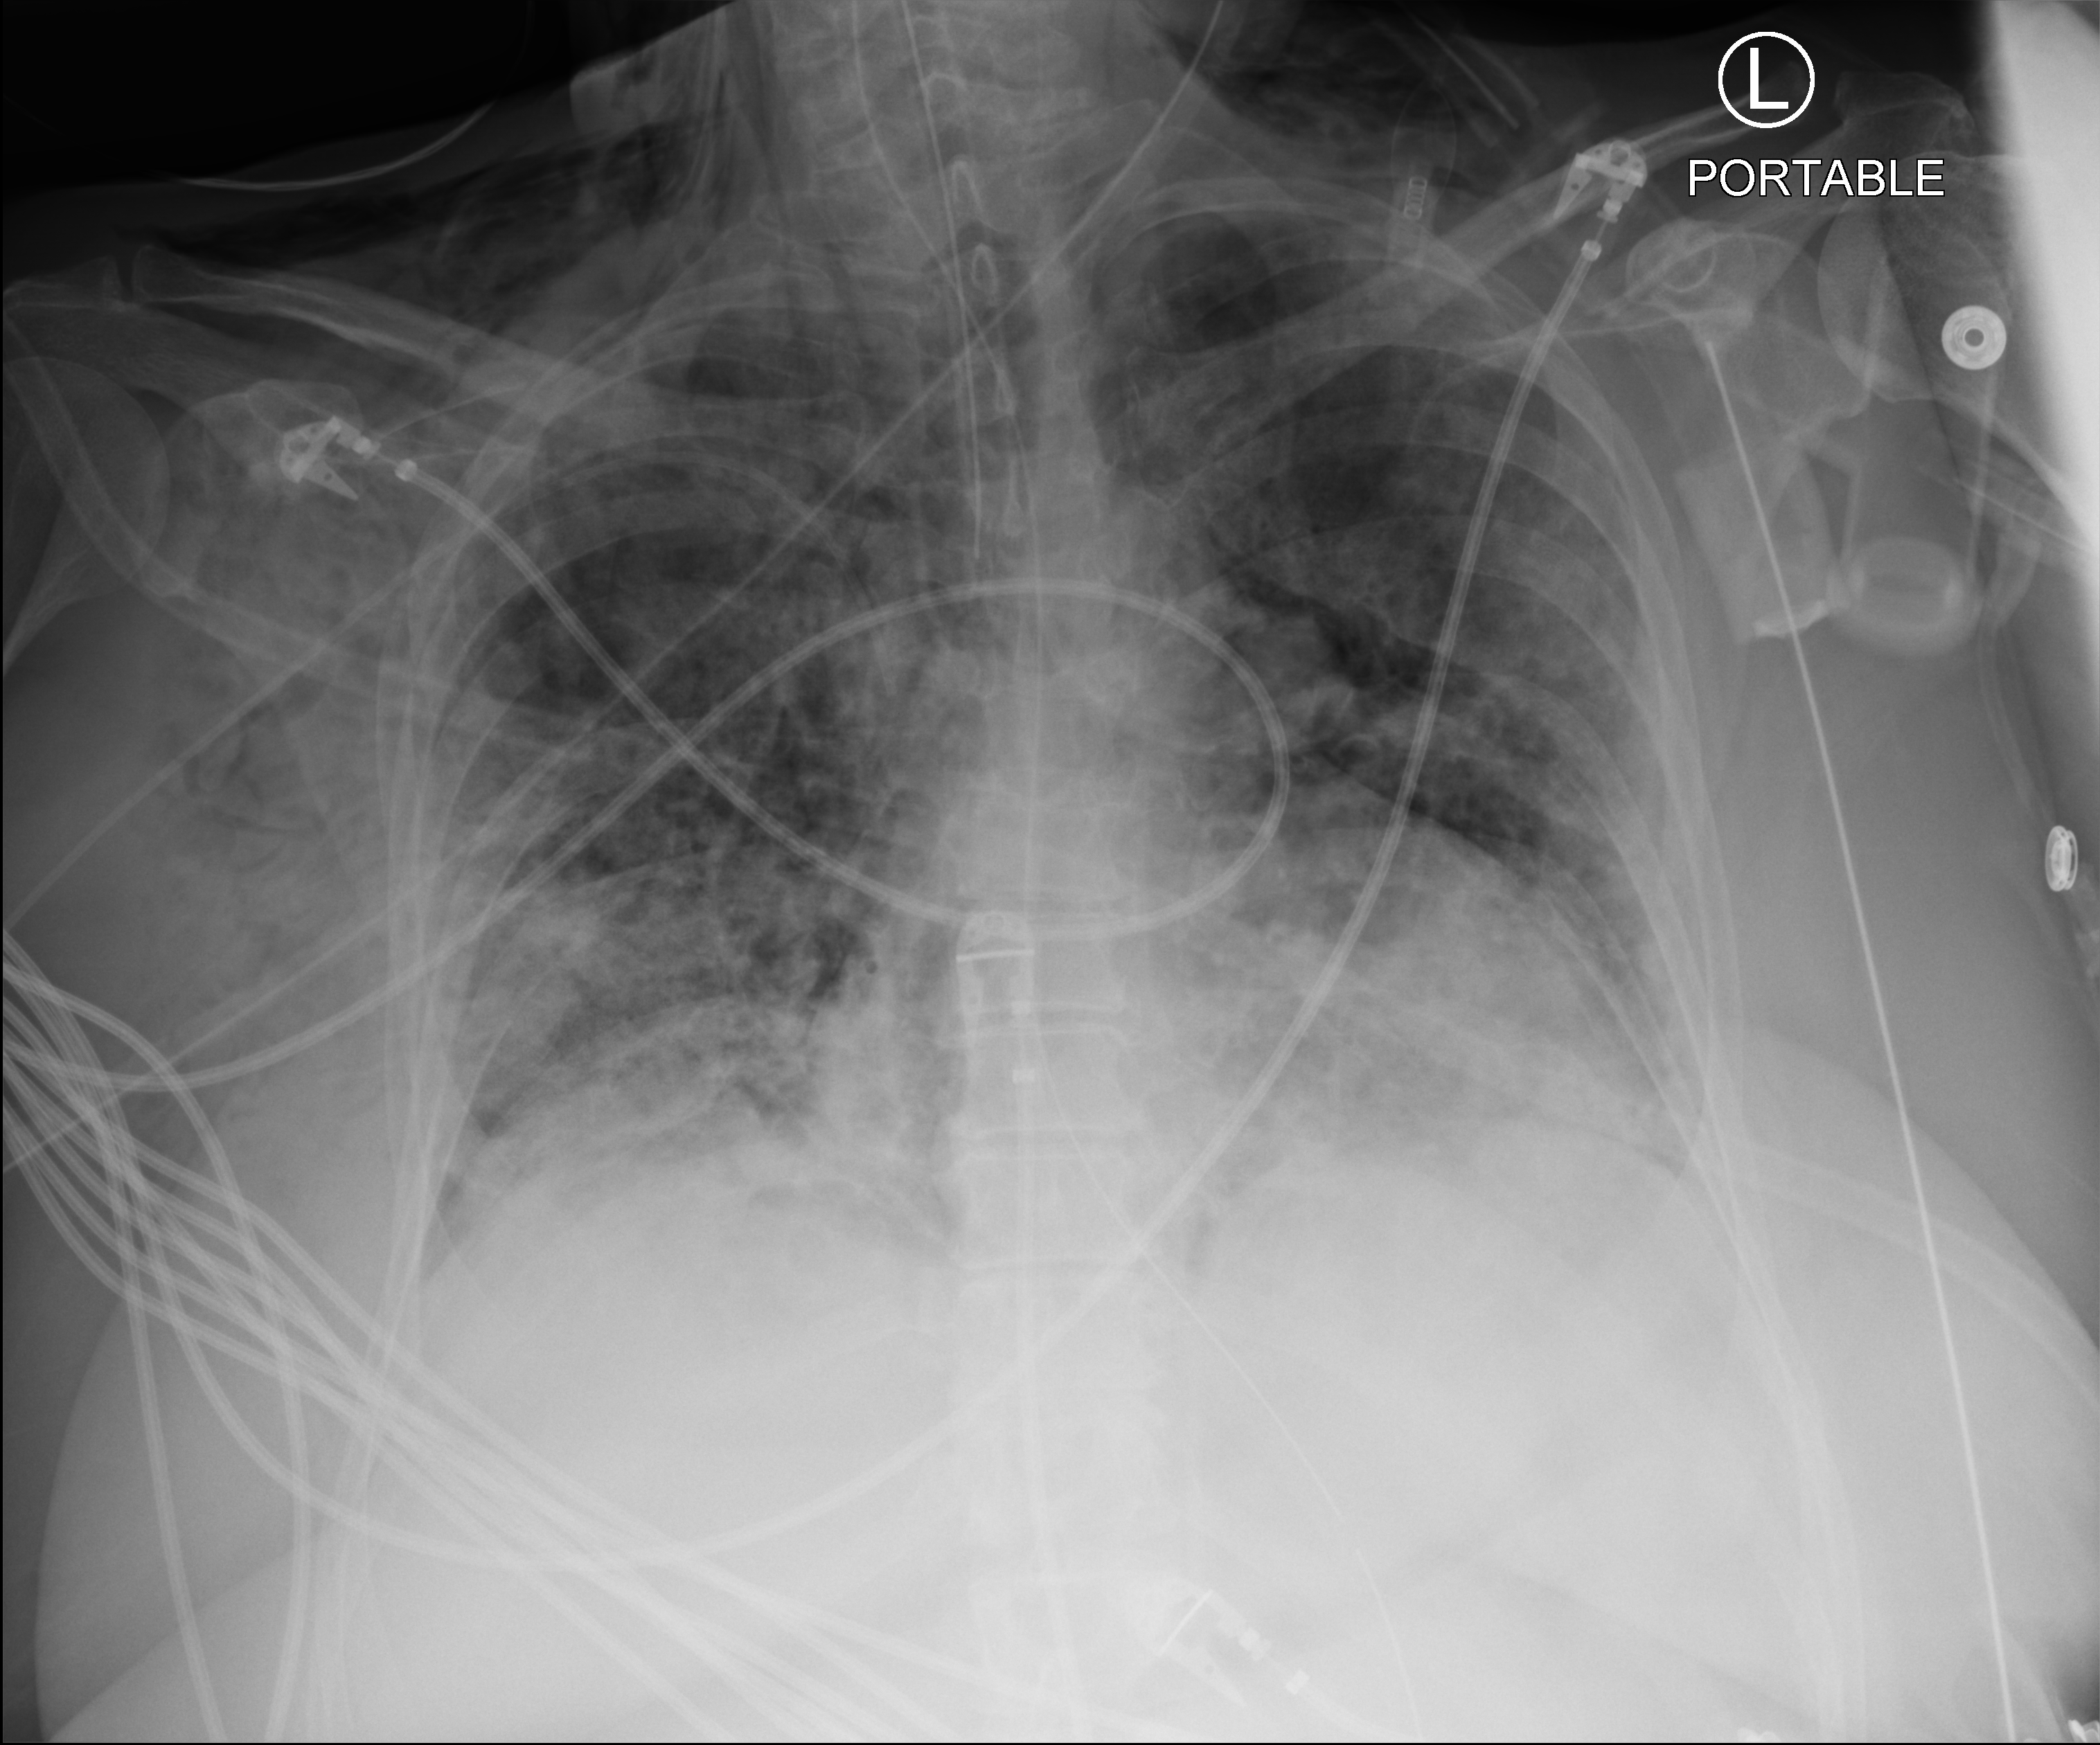
Bedside chest radiograph (computed radiography), anteroposterior (AP) projection. Patient hospitalised with COVID-19; female, aged 60–74 years.
Hospital-stay facts (about this admission, not read from this image; timing relative to this image not recorded):
- other chronic lung disease (admission record): yes
- mechanically ventilated during this hospital stay: yes